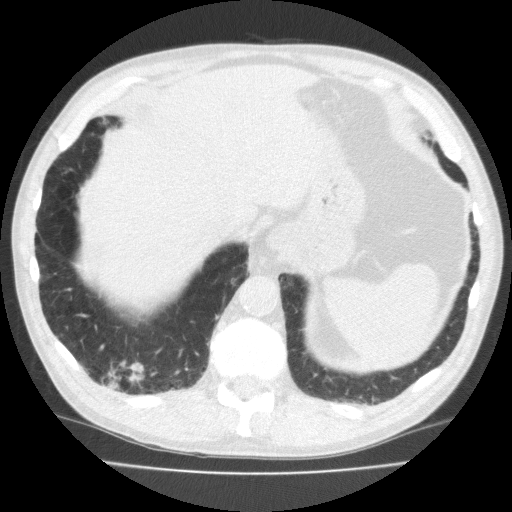
Low-dose screening chest CT, one axial slice; slice 47 of 195 in the series (ordered by position); reconstruction kernel FC10; lung window (W 1500 / L -600 HU); 512 × 512 image matrix, field of view 350 × 350 mm.
Structures marked on this image (outlined manually by an expert reader):
- lesion 1 (tumor, lower lobe of right lung): bounding box <108,360,145,392> (left, top, right, bottom; pixels)